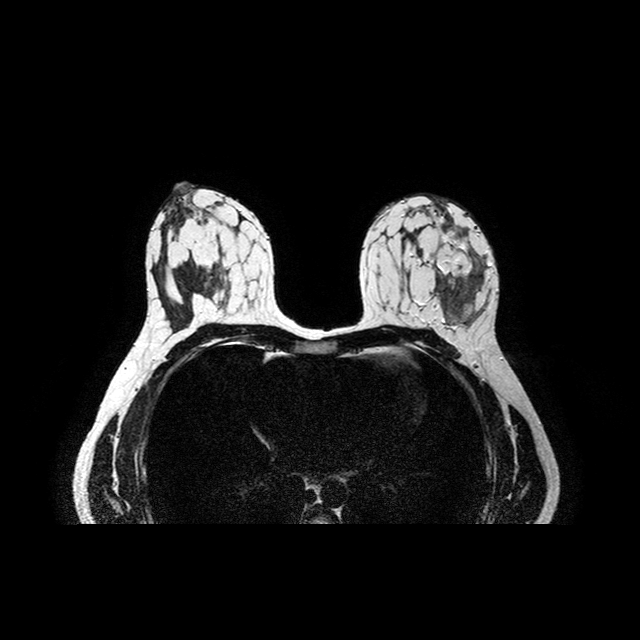
MRI of the breasts; 2 images, each one mid-volume slice chosen by position.
Image 1: fluid-sensitive (T2/STIR) axial slice, series "T2W_TSE SENSE", slice 43 of 84.
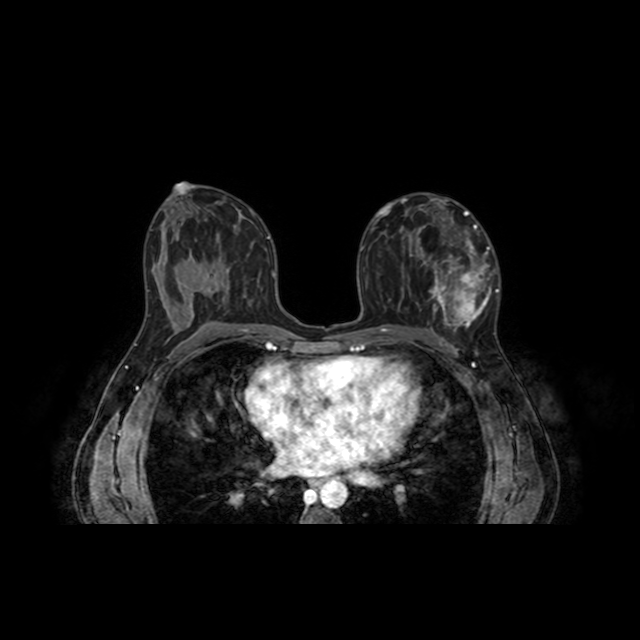
Image 2: post-contrast dynamic axial slice, series "AX BLISS_AUTO SENSE", slice 43 of 84, dynamic phase 5 of 8.
Patient-level pathology facts (from the clinical record, not from the images): pathology diagnosis: benign (right breast).